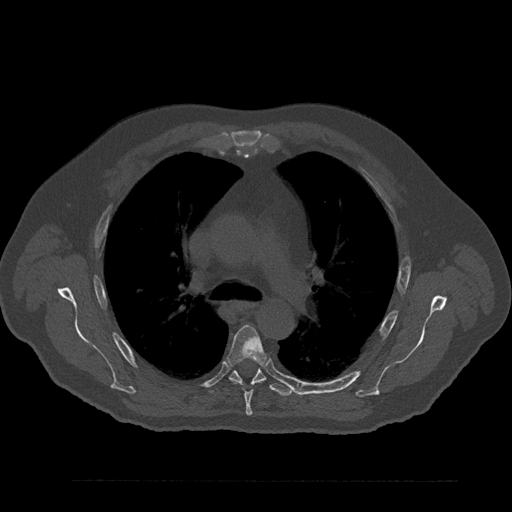
CT including the spine, one axial slice; position 584 of 797 along the scan axis; reconstruction kernel Br40s/3; 120 kVp; bone window (W 1800 / L 400 HU); 0.5 mm slice thickness; 512 × 512 image matrix, field of view 430 × 430 mm. Patient: male, 61 years. Case-level facts recorded for this patient, not image findings: primary cancer: prostate.
Outlined on this slice (semi-automatically segmented with operator editing):
- T5 vertebra: box from (x=227, y=325) to (x=266, y=416) px
- T6 vertebra: (x=211, y=364)–(x=293, y=396)